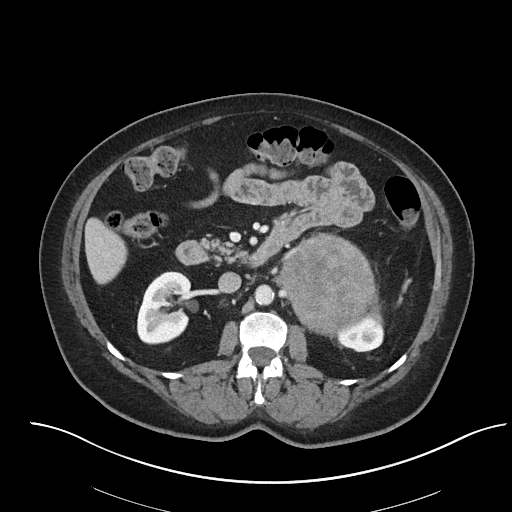
Contrast-enhanced abdominal CT, one axial slice. Slice 34 of 92 in the series (ordered by position). Reconstruction kernel I40f/2. 120 kVp. Soft-tissue window (W 400 / L 40 HU). 512 × 512 image matrix, field of view 440 × 440 mm. Patient: female, 53 years. From the clinical record (not read from this slice): diagnosis: adrenocortical carcinoma; tumour side: left adrenal; tumour size at pathology: 9 cm; Ki-67 index: 28 %; stage (as recorded): 2.
Outlined on this slice (semi-automatically segmented with operator editing):
- mass: bounding box (x1, y1, x2, y2) in pixels: (283, 234, 380, 334)